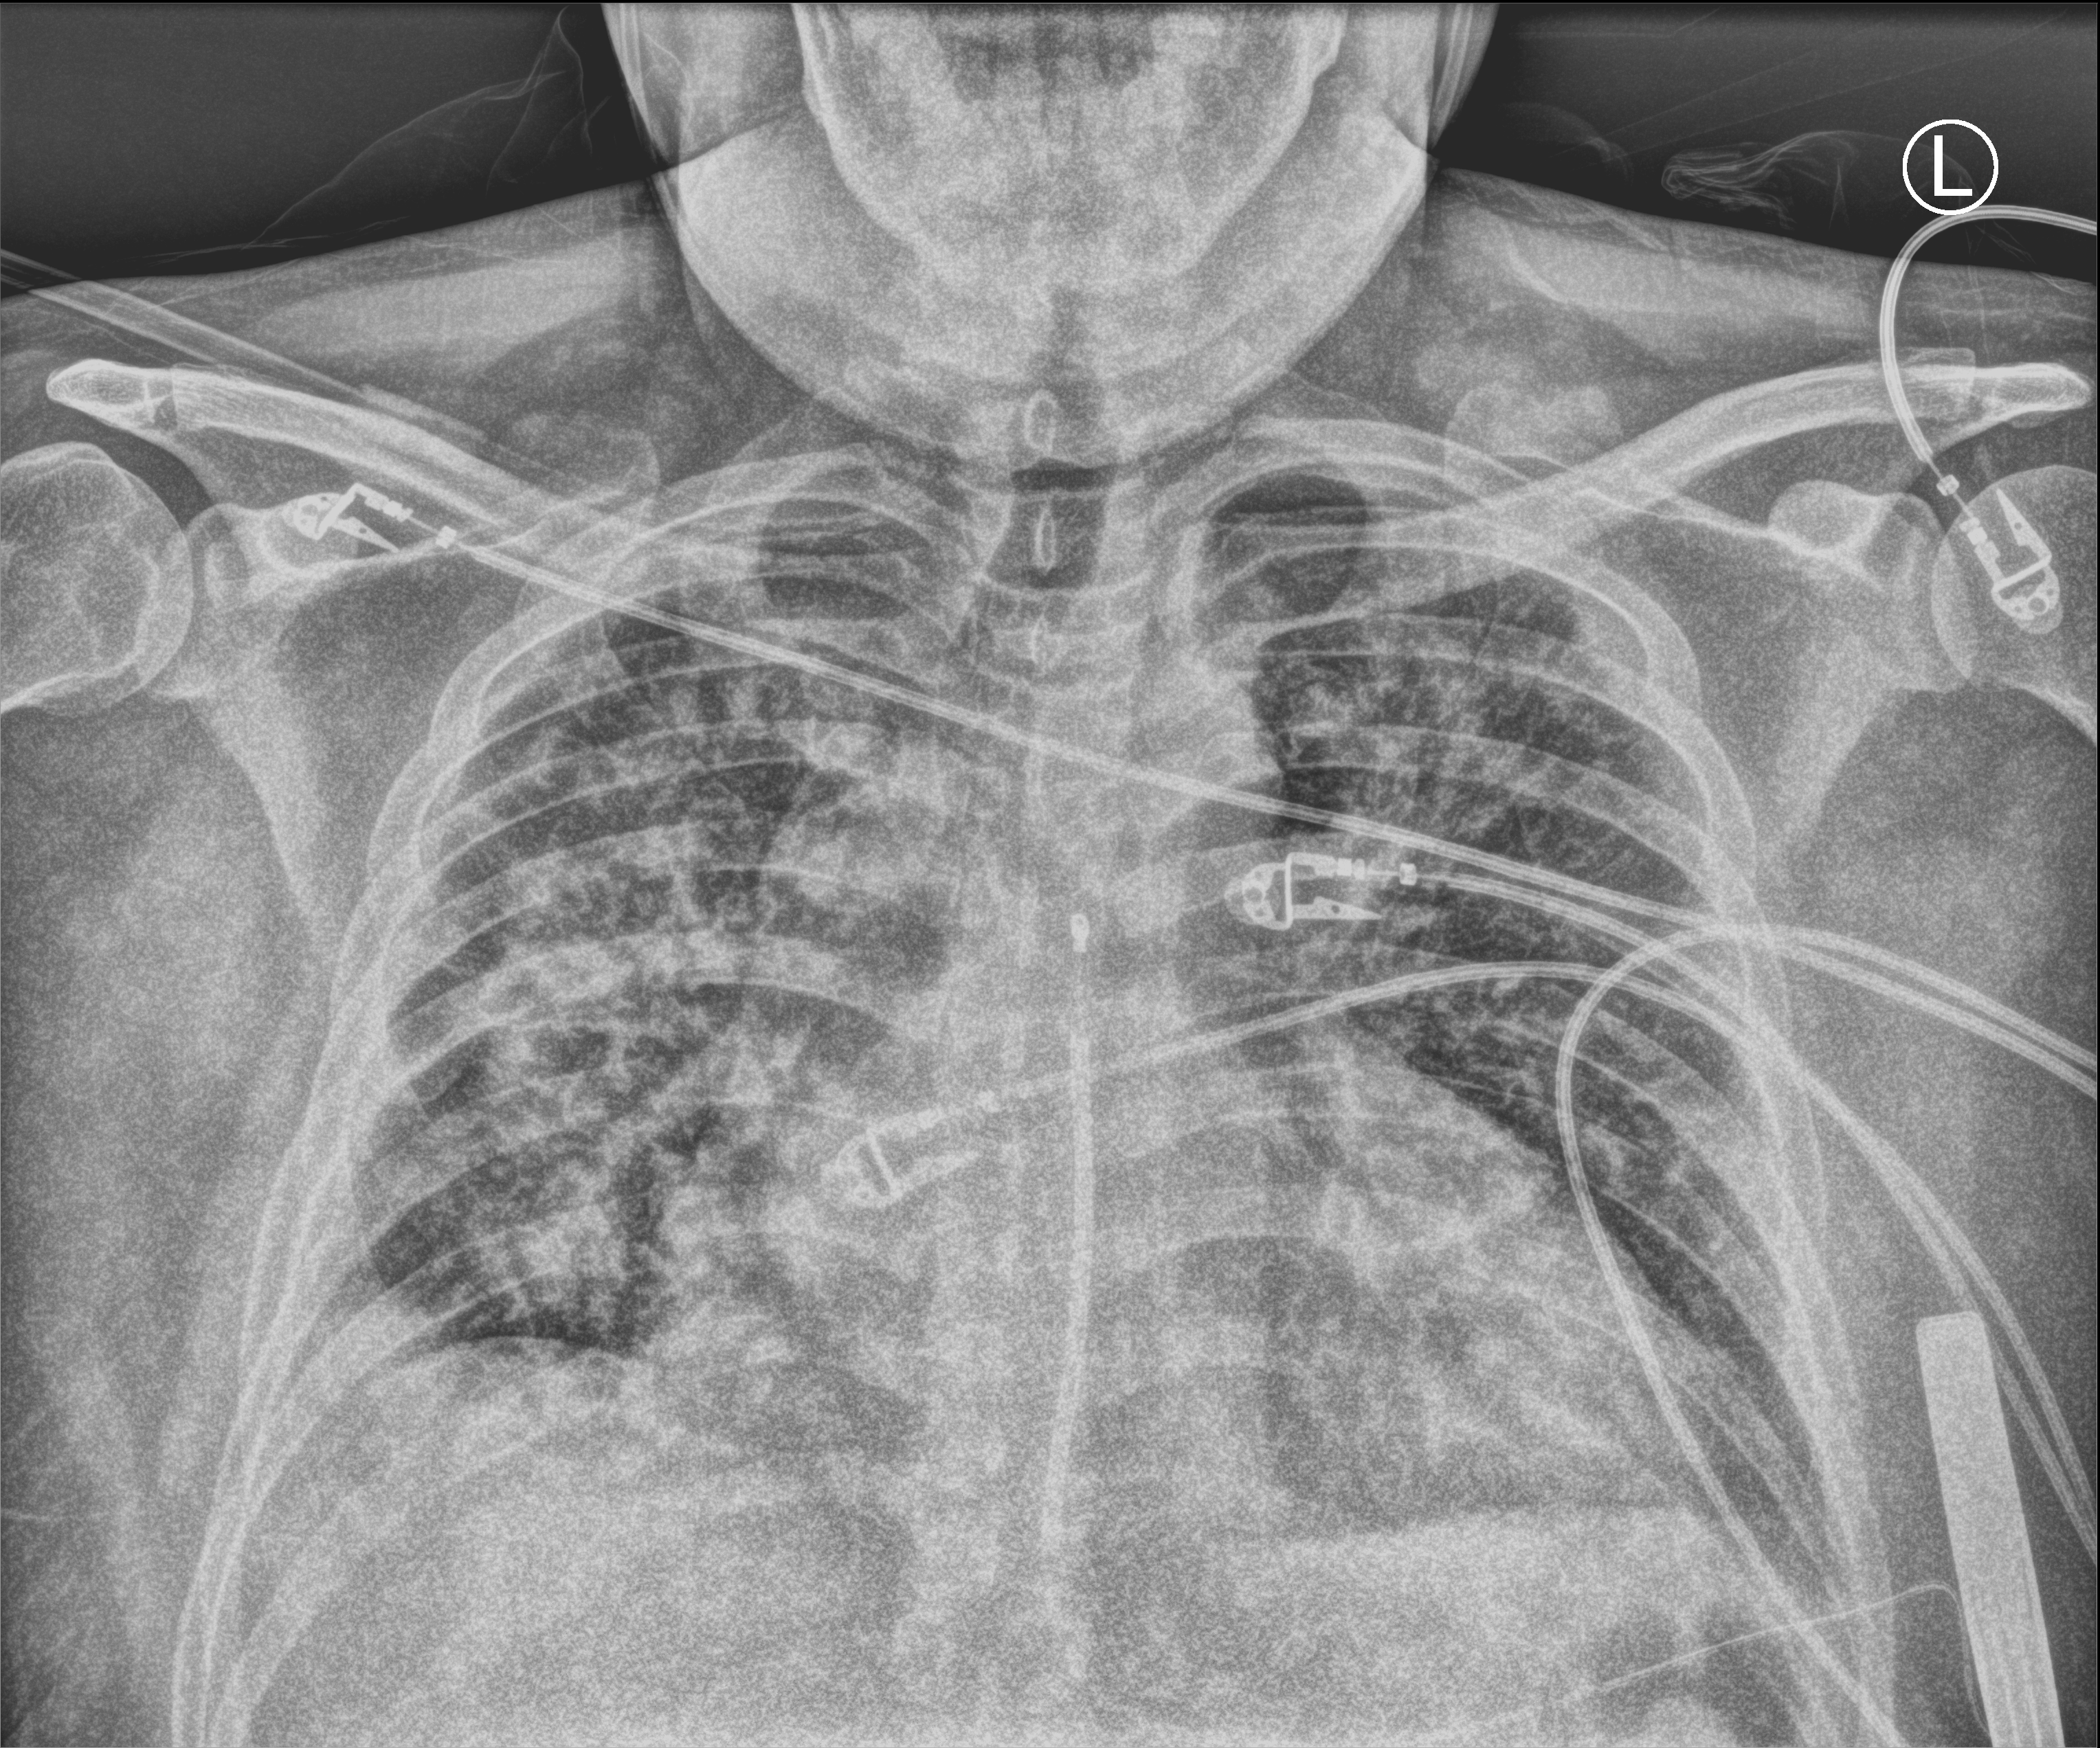
Chest X-ray (portable); anteroposterior (AP) projection. Patient hospitalised with COVID-19; male, aged 18–59 years.
Hospital-stay facts (about this admission, not read from this image; timing relative to this image not recorded):
- mechanically ventilated during this hospital stay: no
- admitted to intensive care during this hospital stay: no